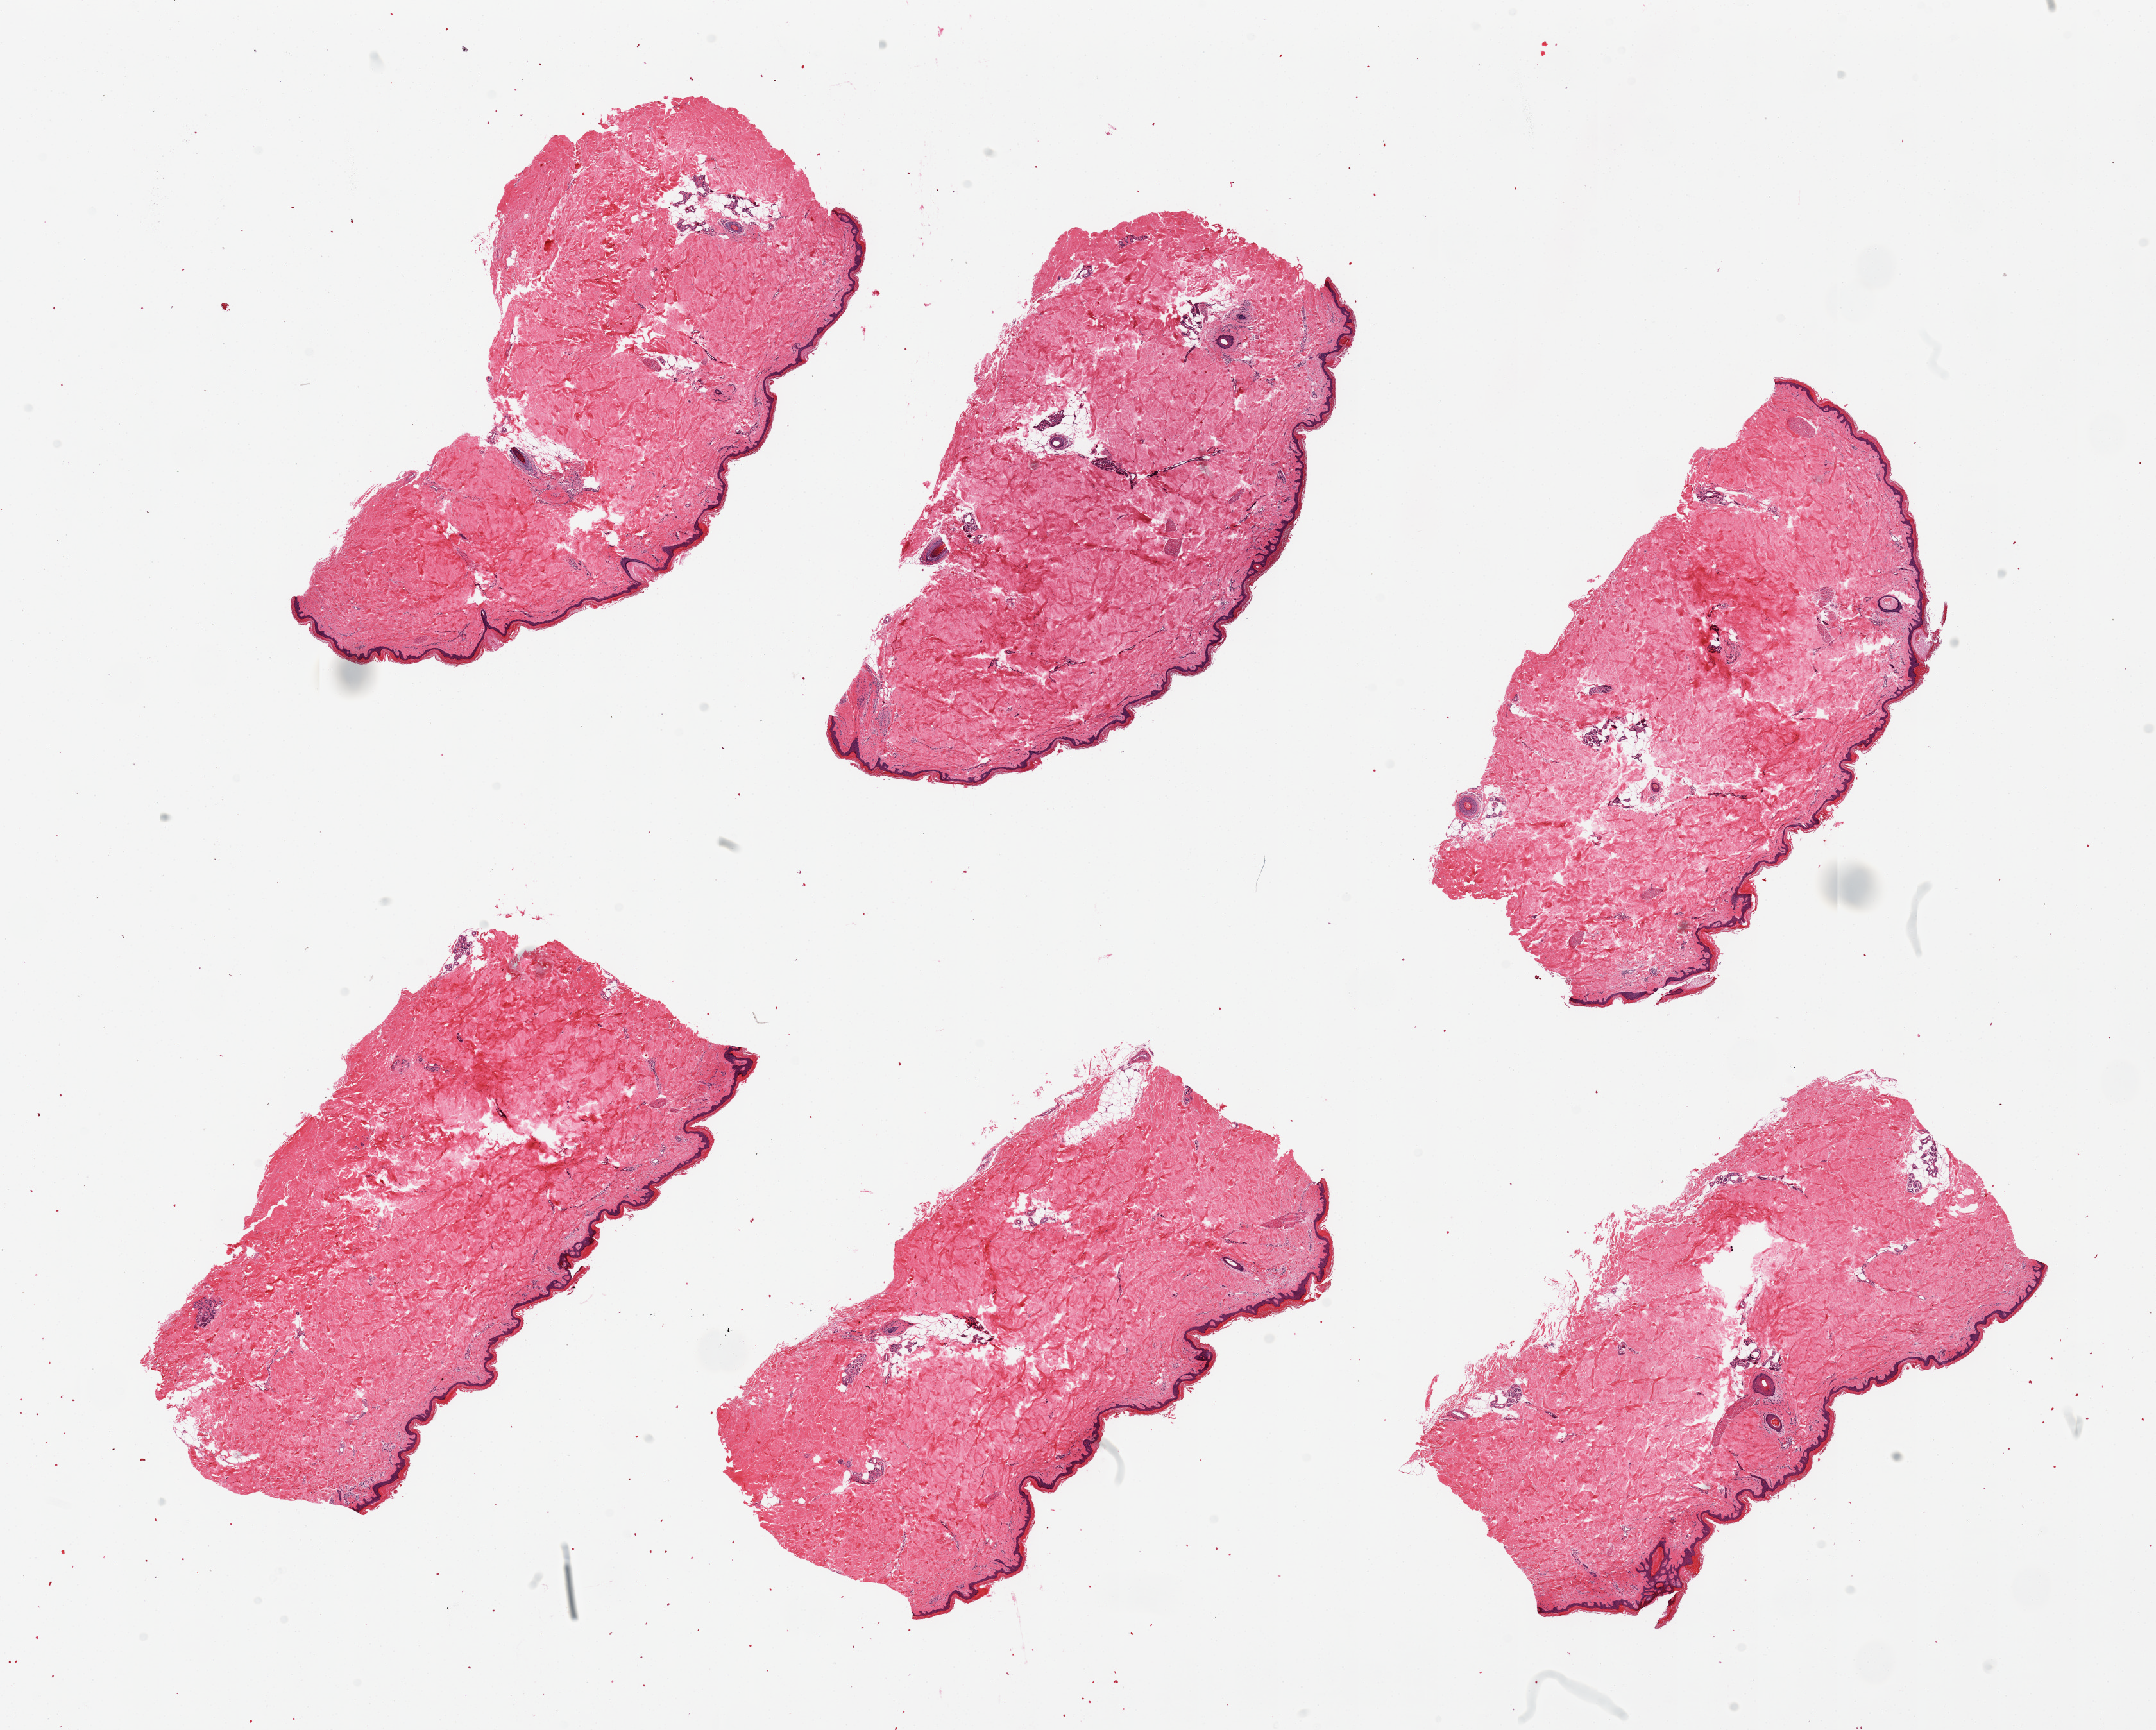
Whole-slide image, hematoxylin and eosin (H&E) stain, brightfield, a low-resolution overview of the entire scanned area, about 26.6 x 21.3 mm (slide scanned at 20x); PAXgene-fixed, paraffin-embedded tissue; sampled site (target tissue): skin of lower leg; donor tissue sample. Donor sex: male.
Pathologist's review note for this sample: 6 pieces, minimal dermal fat; squamous epithelium is ~50microns.